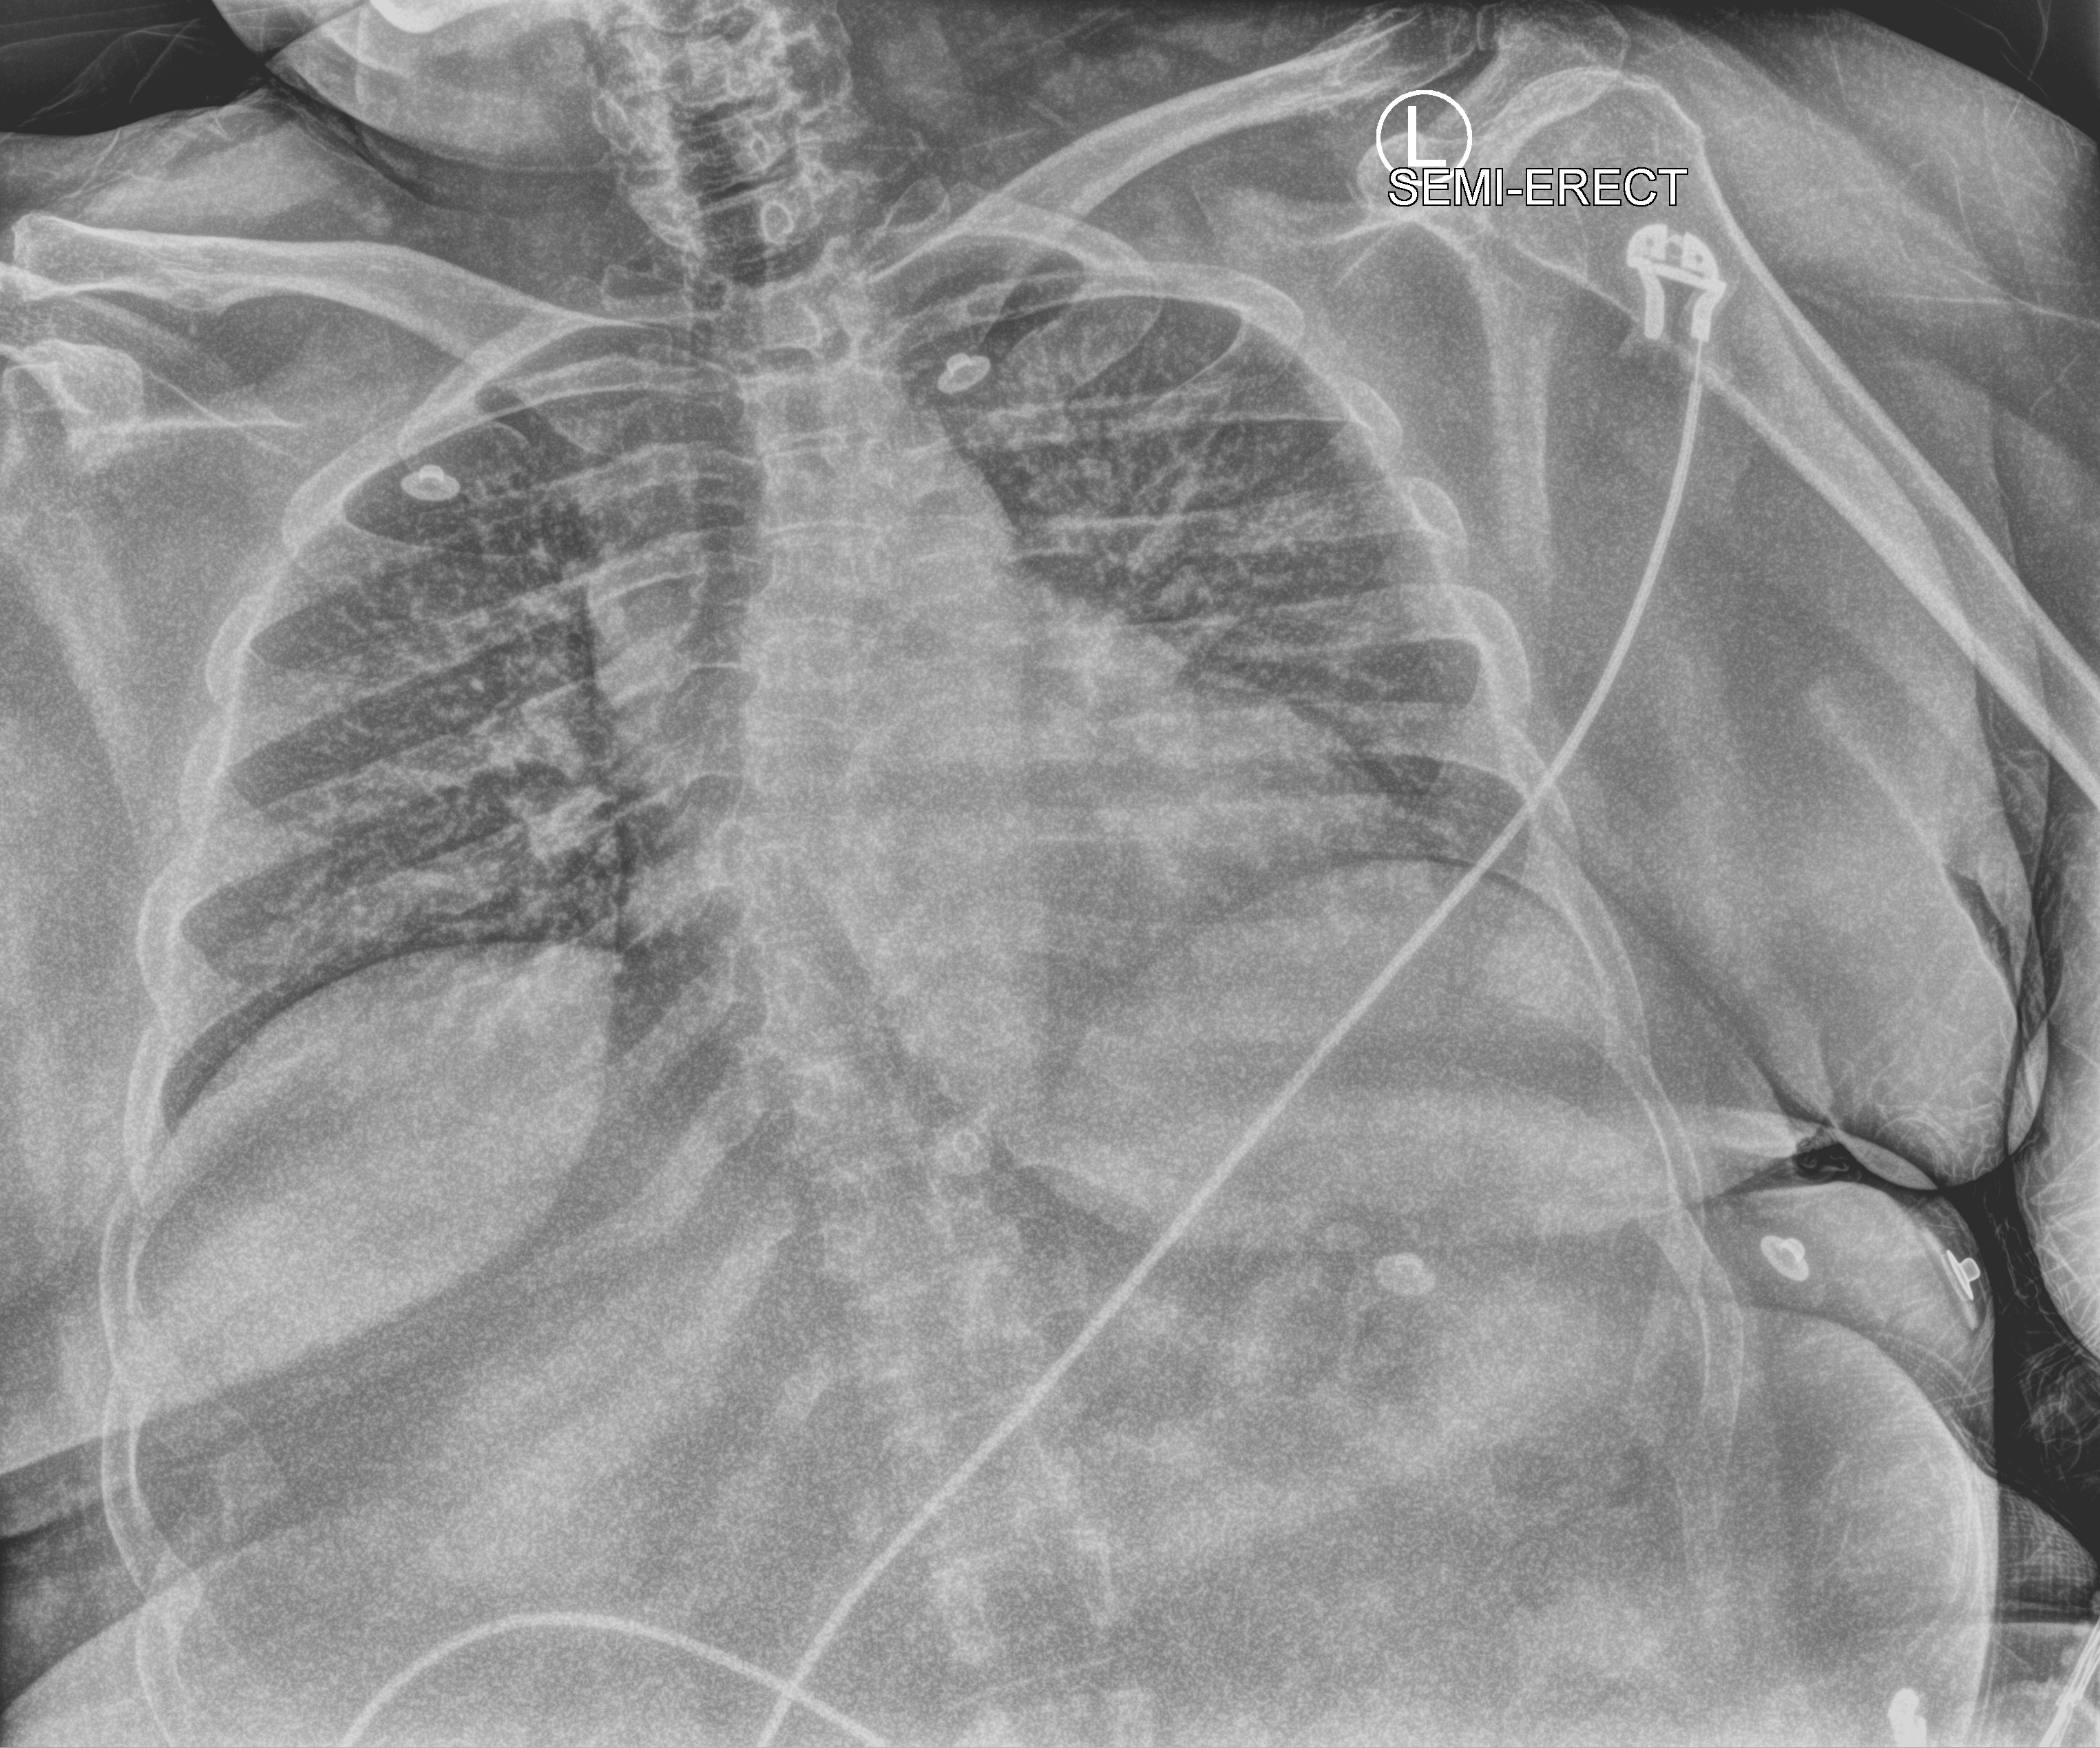
Chest X-ray (portable), anteroposterior (AP) projection. Patient hospitalised with COVID-19; female, aged 18–59 years.
Admission-level facts for this patient (not findings on this image; timing relative to this image not recorded):
- mechanically ventilated during this hospital stay: no